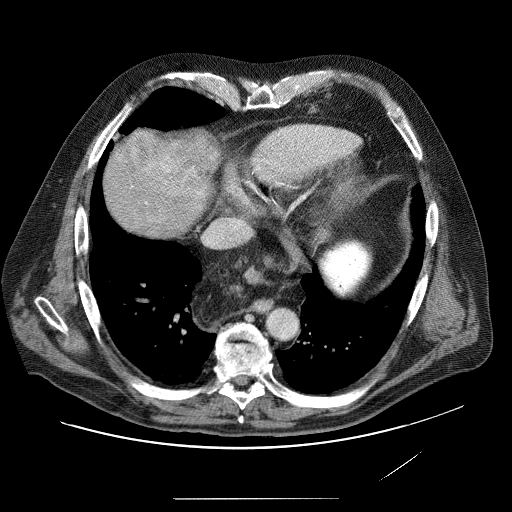
Contrast-enhanced abdominal CT (liver protocol), one axial slice. 120 kVp. Soft-tissue window (W 400 / L 40 HU). 2.5 mm slice thickness. 512 × 512 image matrix. Case-level facts recorded for this patient, not image findings: diagnosis: hepatocellular carcinoma (patient treated with transarterial chemoembolisation; whether this scan precedes or follows treatment is not stated here); TNM stage (as recorded): Stage-IVA.
Structures marked on this image (semi-automatically segmented with operator editing):
- liver parenchyma outside the tumour (the mass and vessels are separate outlines, so this box may not span the whole liver): box from (x=114, y=132) to (x=210, y=222) px
- mass: (x=131, y=135)–(x=212, y=193)